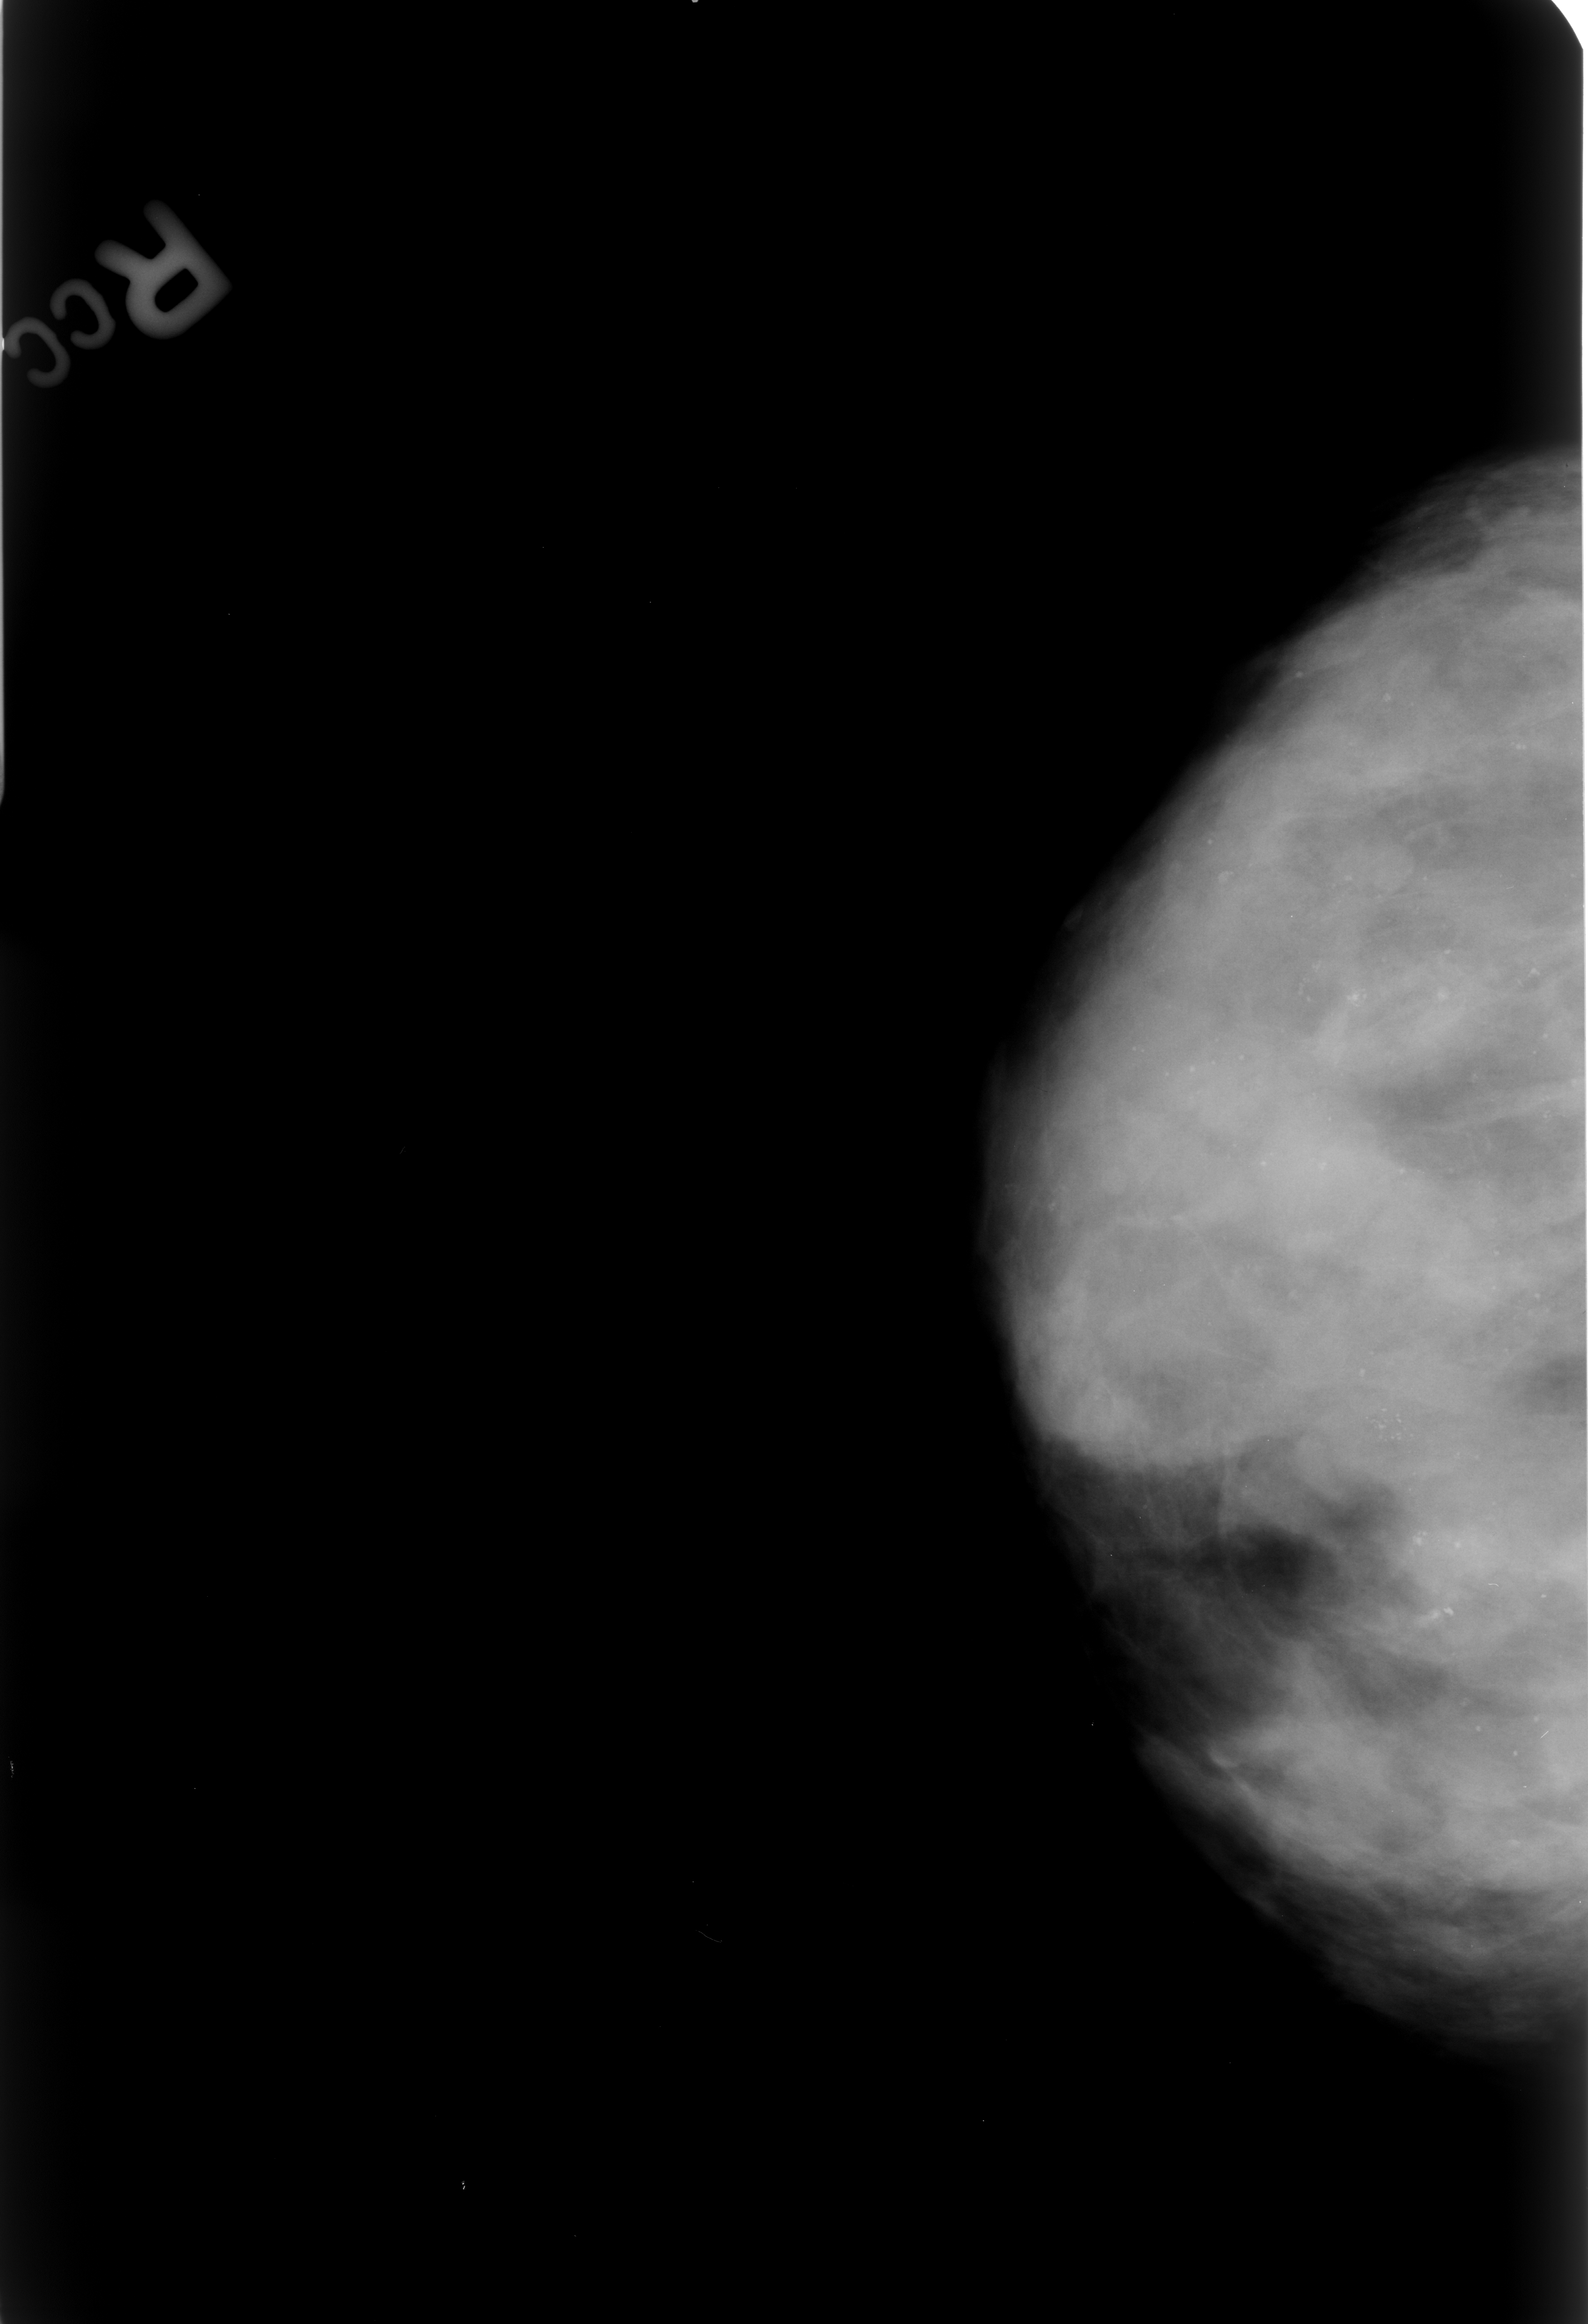
Mammogram (digitized film). Right breast. Craniocaudal (CC) view. Breast composition: extremely dense (BI-RADS density category 4 of 4). 1588 × 2324 image matrix.
Expert-marked regions of interest on this film, with their recorded descriptors:
- calcifications, morphology punctate / pleomorphic, distribution clustered; BI-RADS assessment category 4; pathology (as recorded): benign: bounding box [x1, y1, x2, y2] px = [1317, 1354, 1438, 1478]